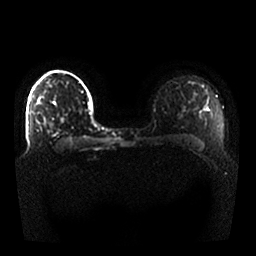
Breast MRI, one axial slice; position 19 of 25 along the scan axis; diffusion-weighted series; image 2 of 4 stored at this slice position (different b-values; order by instance number); 1.5 T; 4 mm slice thickness; 256 × 256 image matrix. Female patient.
Structures marked on this image (expert manual segmentation):
- tumour on diffusion-weighted imaging: bounding box <52,135,54,137> (left, top, right, bottom; pixels)